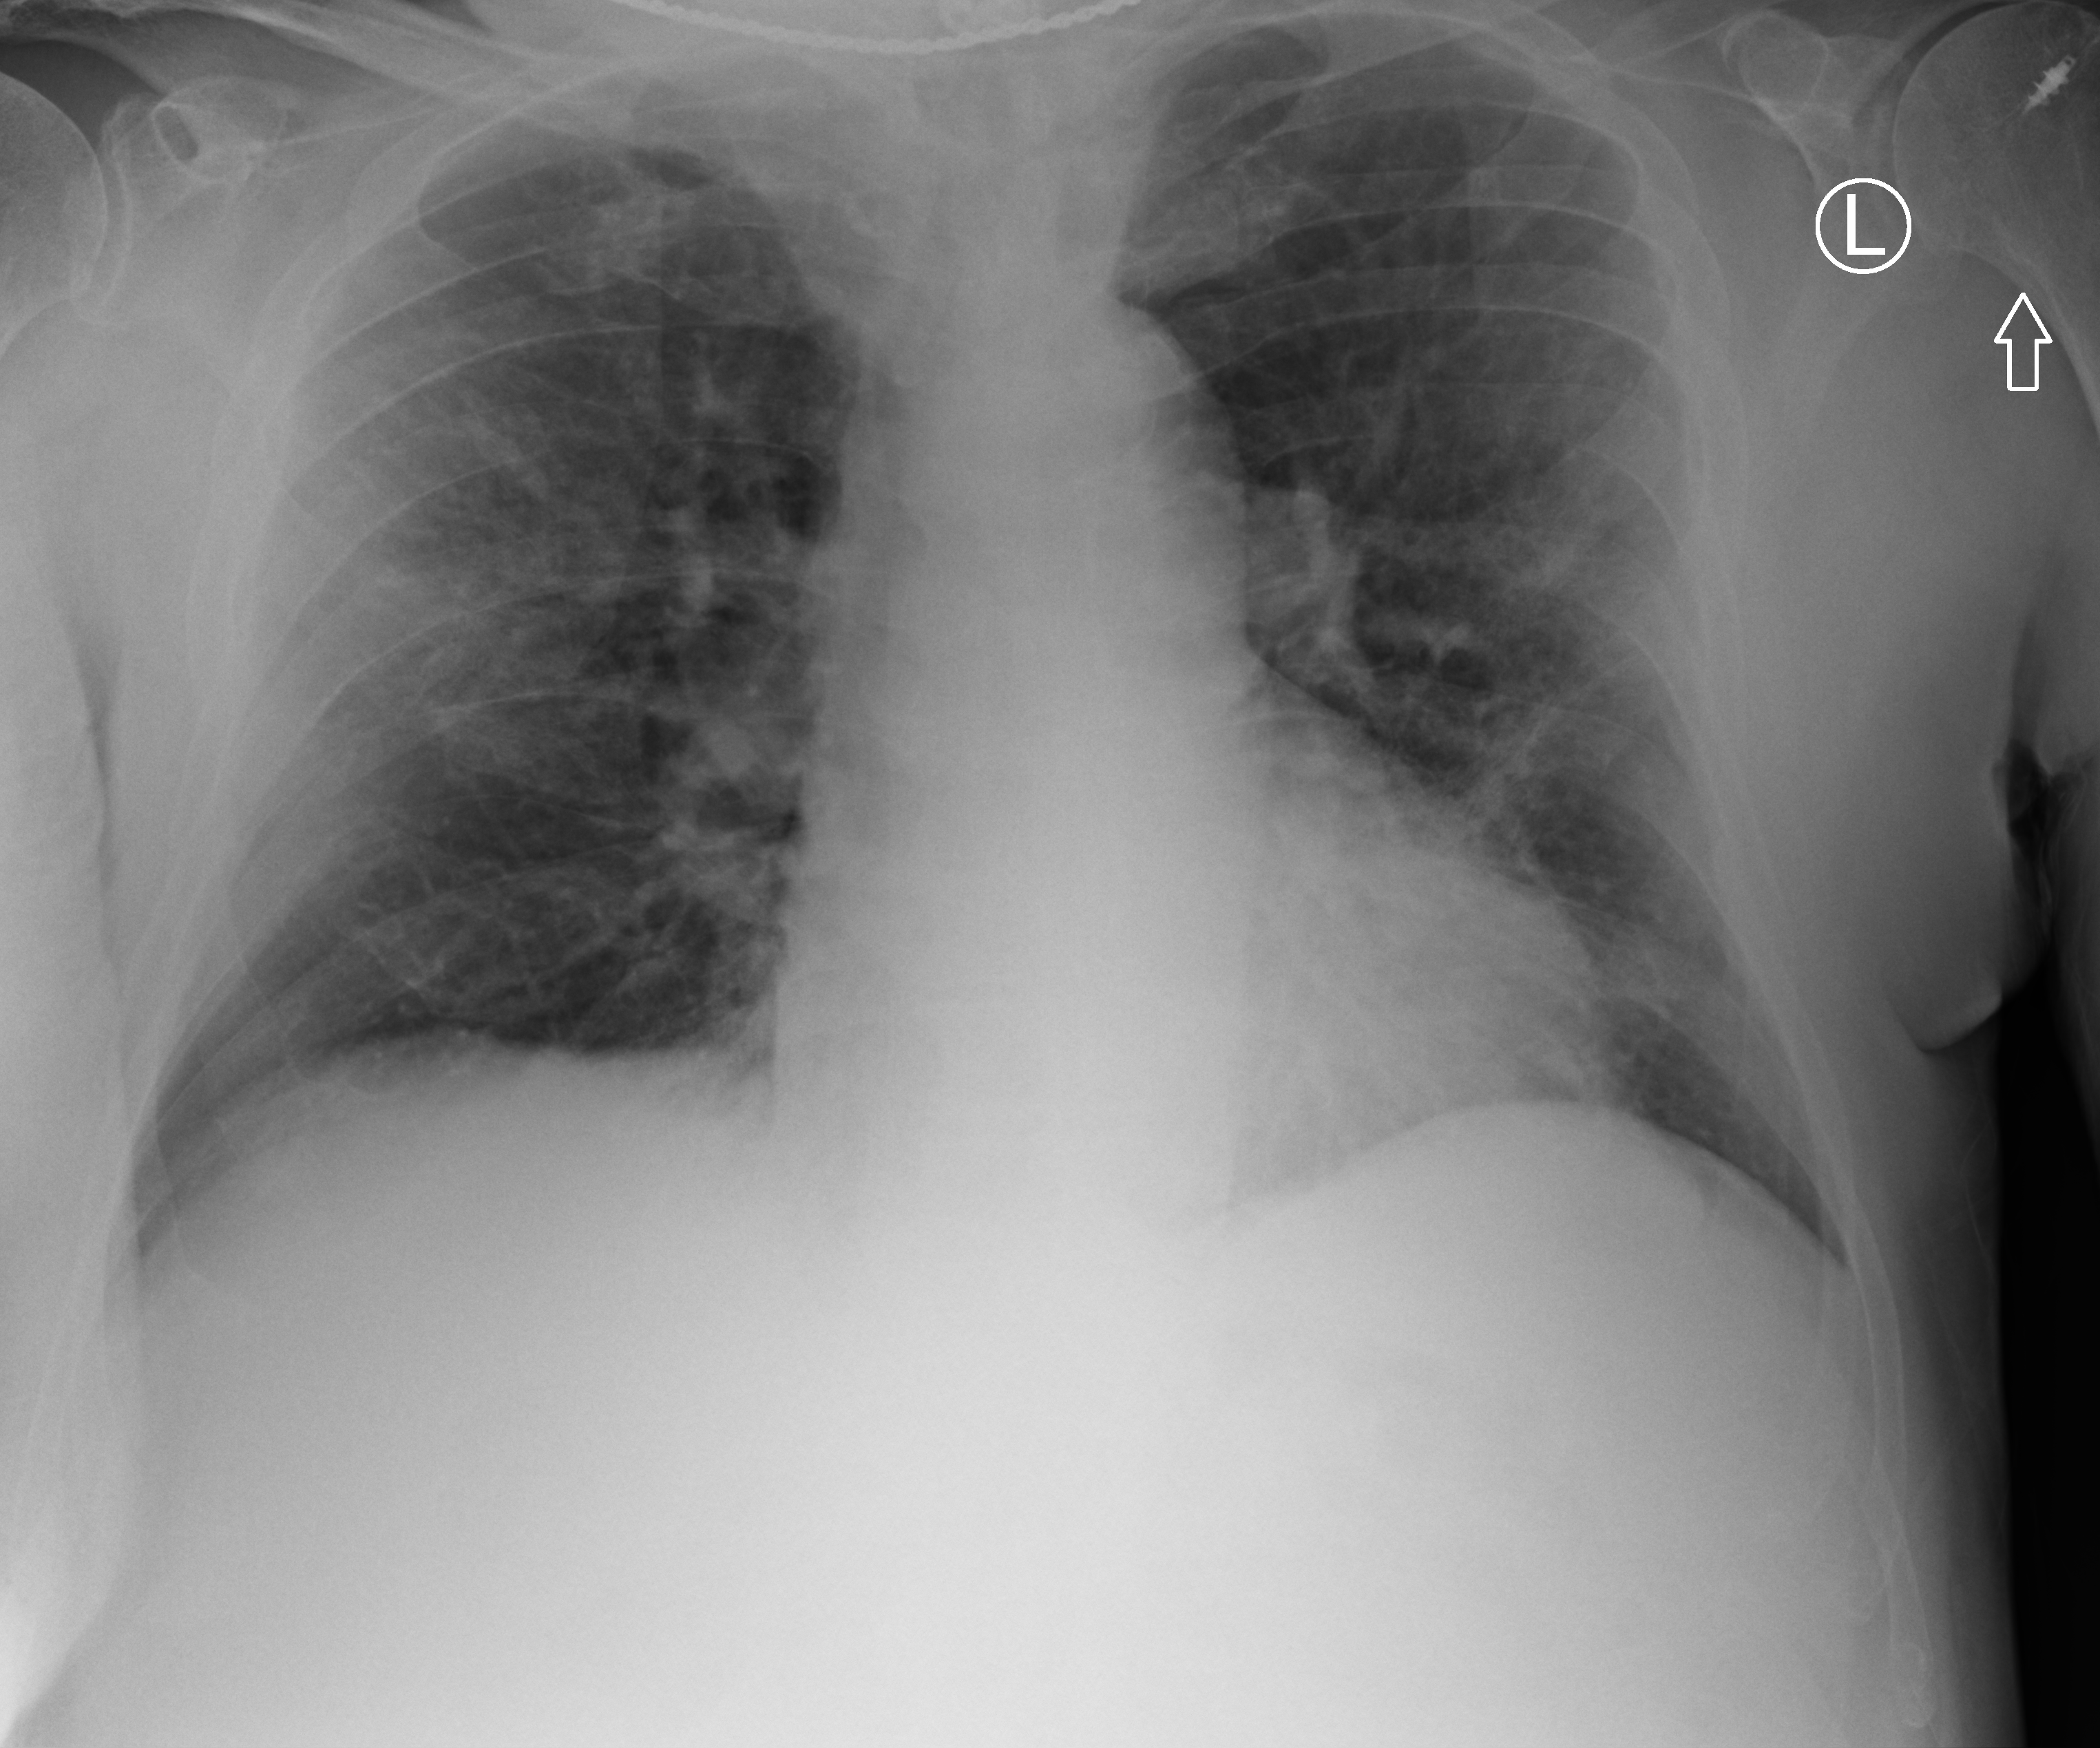
Bedside chest radiograph (computed radiography). Male patient hospitalised with COVID-19, age 75–90 years.
Admission-level facts for this patient (not findings on this image; timing relative to this image not recorded): admitted to intensive care during this hospital stay: yes; length of hospital stay: 26 days.